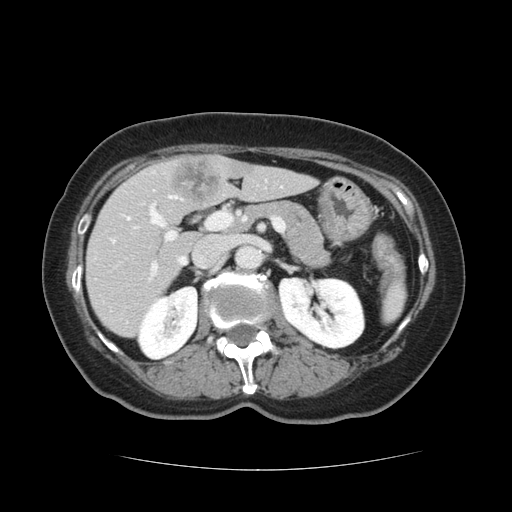
Contrast-enhanced abdominal CT, one axial slice. Position 62 of 128 along the scan axis. 120 kVp. Intravenous contrast given. Soft-tissue window (W 400 / L 40 HU). 2.5 mm slice thickness. 512 × 512 image matrix, field of view 366 × 366 mm. Female patient, age 67 years. Case-level facts recorded for this patient, not image findings: diagnosis: colorectal cancer liver metastases, imaged before liver resection; multiple liver metastases: yes; largest metastasis: 3 cm.
Structures marked on this image (expert manual segmentation):
- hepatic veins: bounding box [x1, y1, x2, y2] px = [129, 196, 185, 265]
- liver: [87, 156, 314, 337]
- planned liver remnant (the part of the liver to remain after resection): [87, 165, 314, 338]
- portal vein (with intrahepatic branches): [112, 179, 268, 280]
- liver metastasis: [169, 160, 220, 203]